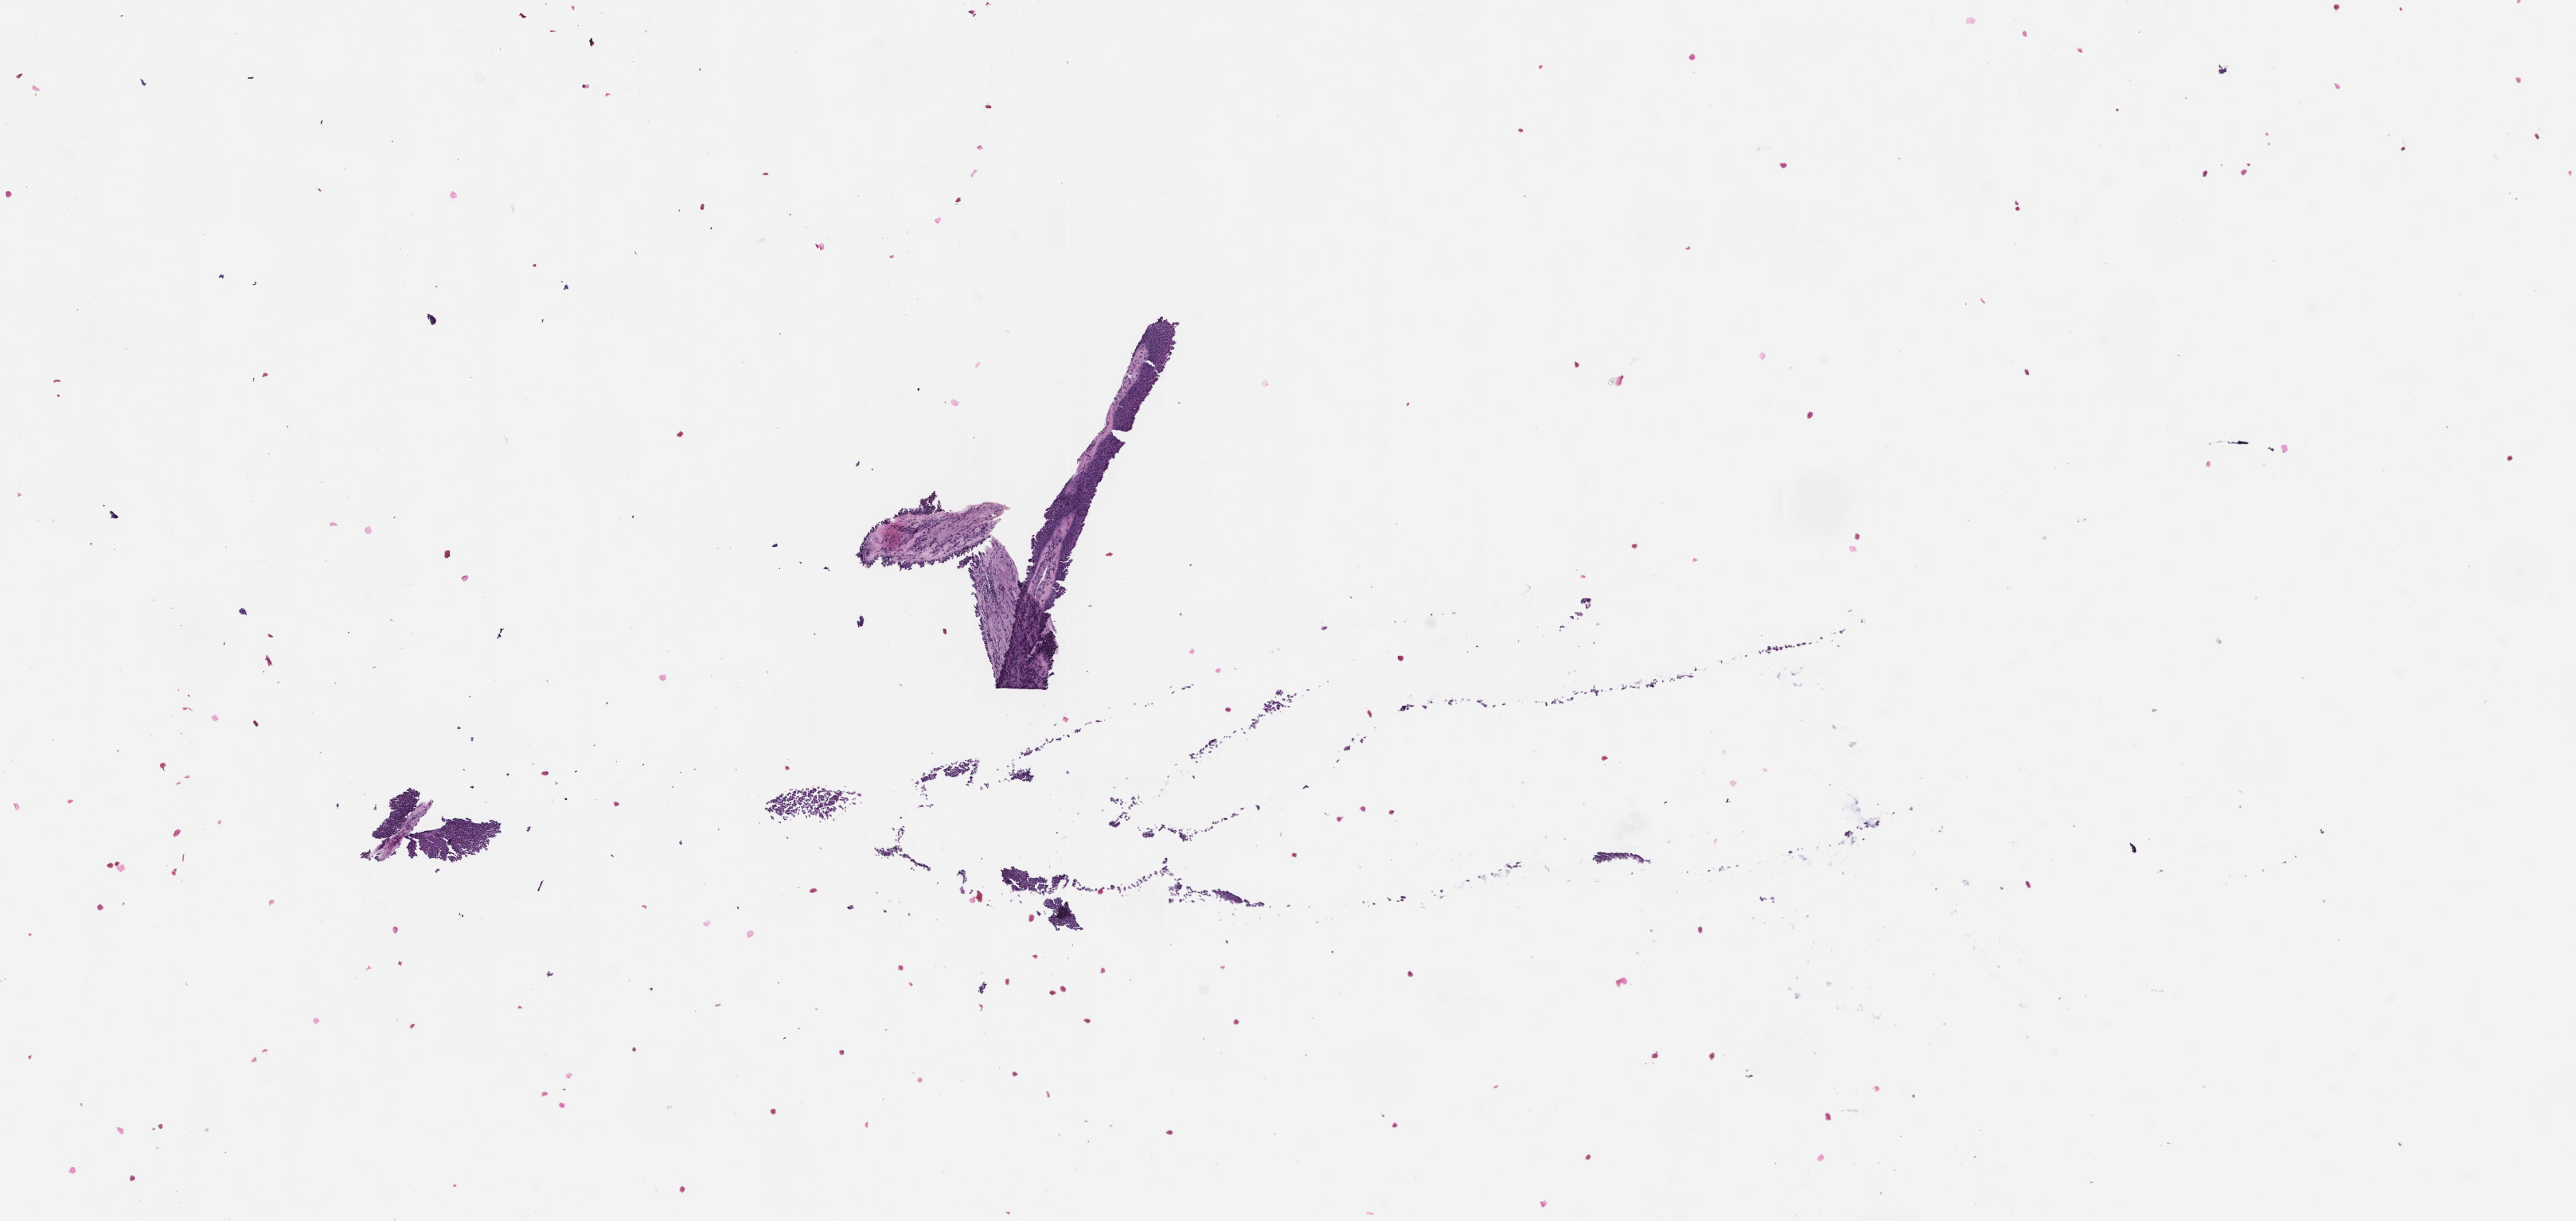
H&E whole-slide image, low-resolution overview of the scanned area, about 13.1 x 6.2 mm; formalin-fixed paraffin-embedded section; tissue site: lung; archival tissue. Patient: male.
• this section: primary tumor
• diagnosis: Small Cell Lung Carcinoma